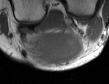
MRI of an extremity soft-tissue mass, one axial slice. Position 16 of 50 along the scan axis. MR volume resampled by the dataset authors to the PET/CT grid (not the native acquisition matrix). 3.27 mm slice thickness. 109 × 84 image matrix, field of view 106 × 82 mm. Male patient. Case-level facts recorded for this patient, not image findings: histological type: synovial sarcoma; site of the primary tumour: left poplietal fossa.
Outlined on this slice (expert contour drawn on MRI and transferred to this co-registered scan by the dataset authors):
- gross tumour volume (mass): bounding box (x1, y1, x2, y2) in pixels: (25, 30, 81, 65)